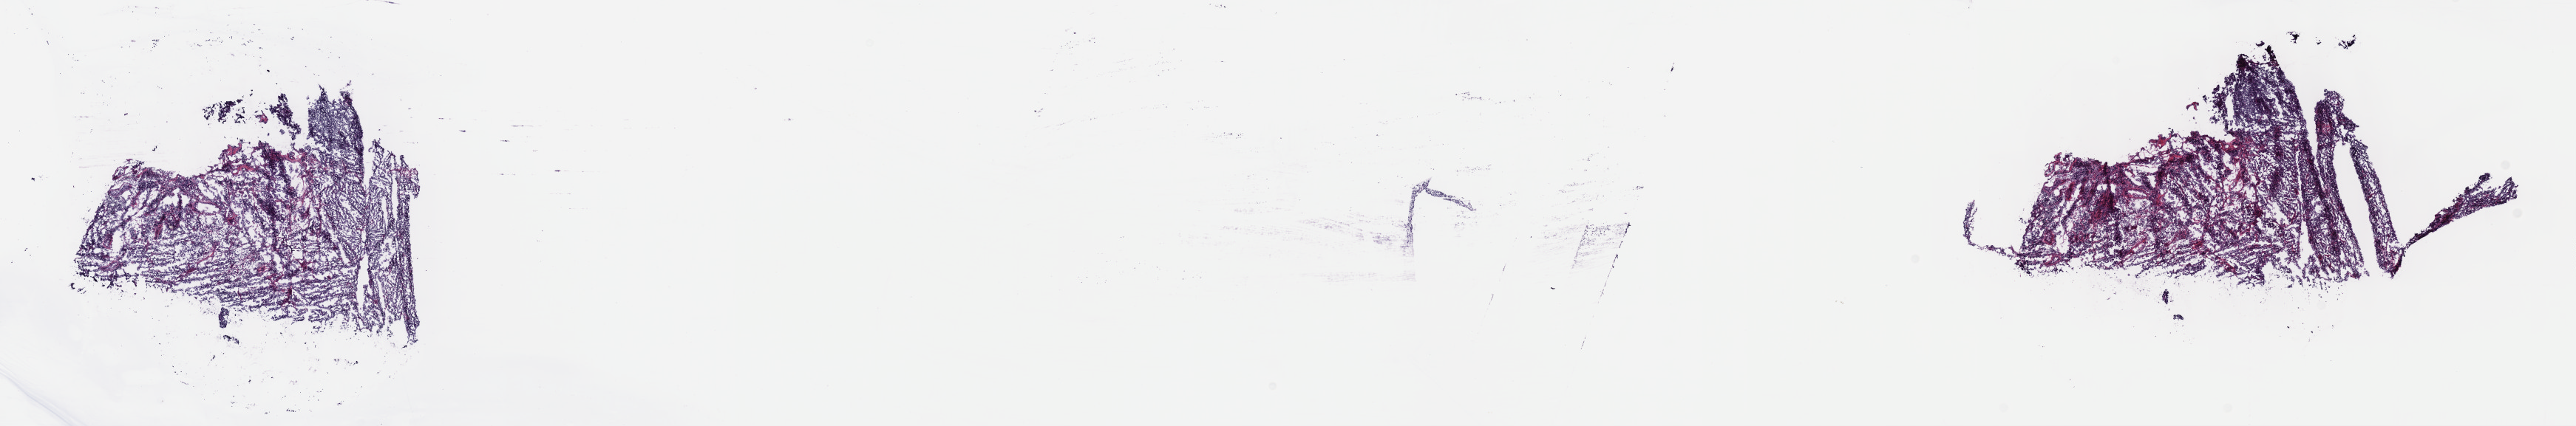
Digitized Hematoxylin and eosin (H&E) stained tissue section (whole slide) — whole scanned area (about 28.2 x 4.7 mm) shown as a low-resolution overview; frozen section from the top of the tissue portion; primary tumour sample from the testis. Patient: male, age at initial diagnosis 39 years. Pathologist review of this section (percent, as recorded): tumour cells 100%, tumour nuclei 65%, normal cells 0%, stromal cells 0%, necrosis 0%. Inflammatory infiltration, as recorded: lymphocyte infiltration 0%, monocyte infiltration 0%, neutrophil infiltration 0%.
* AJCC pathologic stage: IA
* TNM: T1 NX M0
* histologic diagnosis: Seminoma, NOS